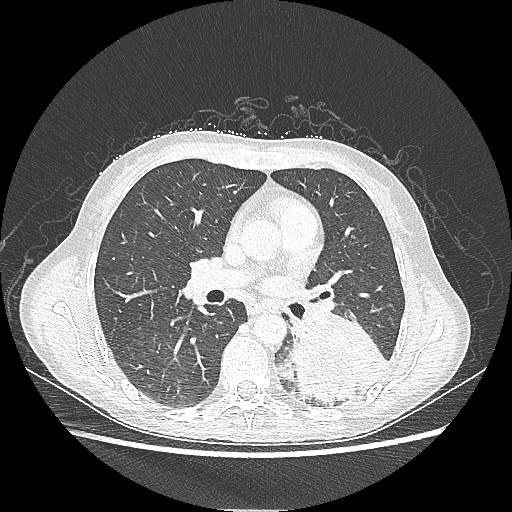
Chest CT, one axial slice. Position 121 of 220 along the scan axis. Lung window (W 1500 / L -600 HU). 512 × 512 image matrix, field of view 360 × 360 mm. Patient: female, 53 years. Case-level facts recorded for this patient, not image findings: clinical TNM (as recorded): T3 N0 M0.
Annotated regions visible in this slice (rectangle marked by the reading radiologist):
- lung tumour (recorded histology: adenocarcinoma): bounding box [x1, y1, x2, y2] px = [290, 307, 390, 403]